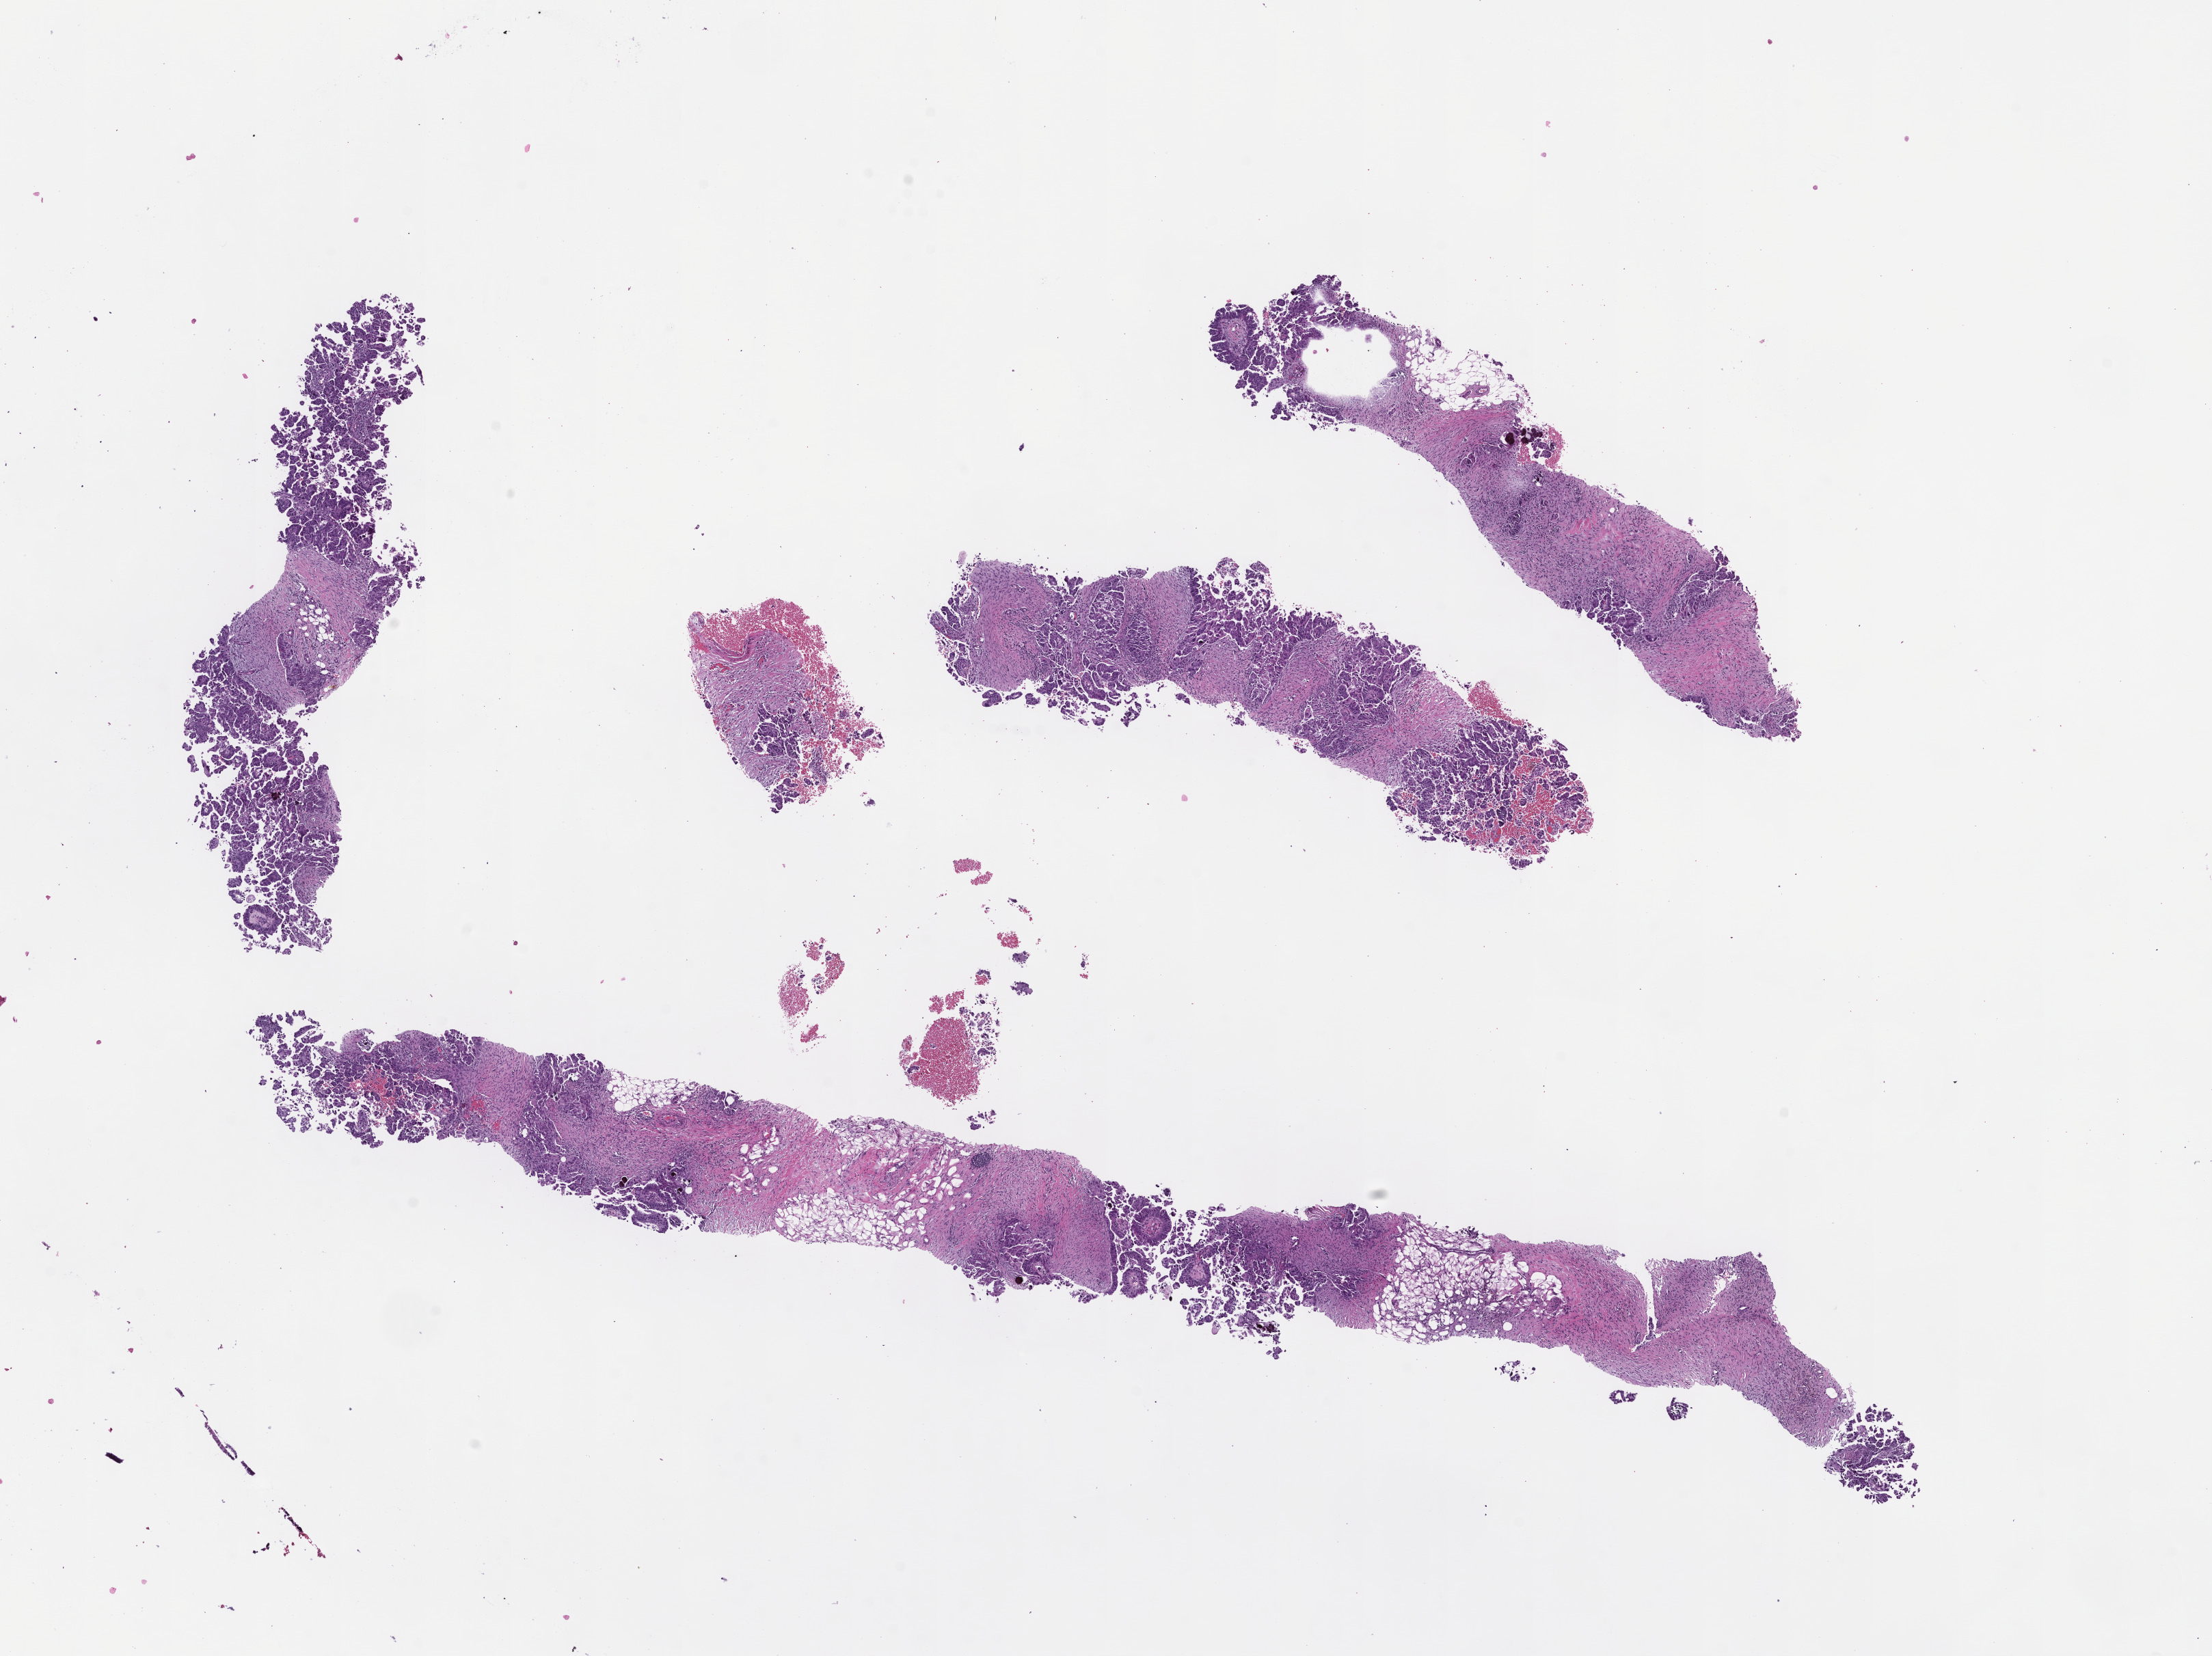
Hematoxylin and eosin (H&E) whole-slide image — a low-resolution overview of the entire scanned area, about 13.1 x 9.8 mm. Formalin-fixed, paraffin-embedded (FFPE) tissue. Site: ovary. Archival tissue. Patient: female.
• this section: primary tumor
• diagnosis: Ovarian Carcinoma